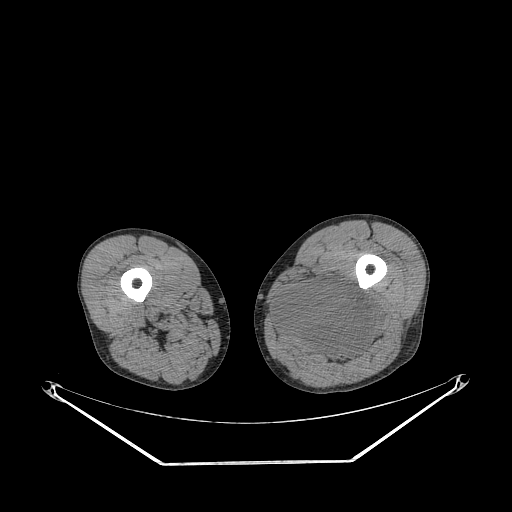
CT of an extremity soft-tissue mass (from a PET/CT study), one axial slice. Reconstruction kernel STANDARD. Soft-tissue window (W 400 / L 40 HU). 3.75 mm slice thickness. 512 × 512 image matrix, field of view 500 × 500 mm. Male patient. From the clinical record (not read from this slice): histological type: undifferentiated pleomorphic liposarcoma; grade: high; site of the primary tumour: left thigh.
Outlined on this slice (expert contour drawn on MRI and transferred to this co-registered scan by the dataset authors):
- gross tumour volume including surrounding oedema: bounding box [x1, y1, x2, y2] px = [276, 279, 380, 362]
- gross tumour volume (mass): [276, 279, 380, 360]